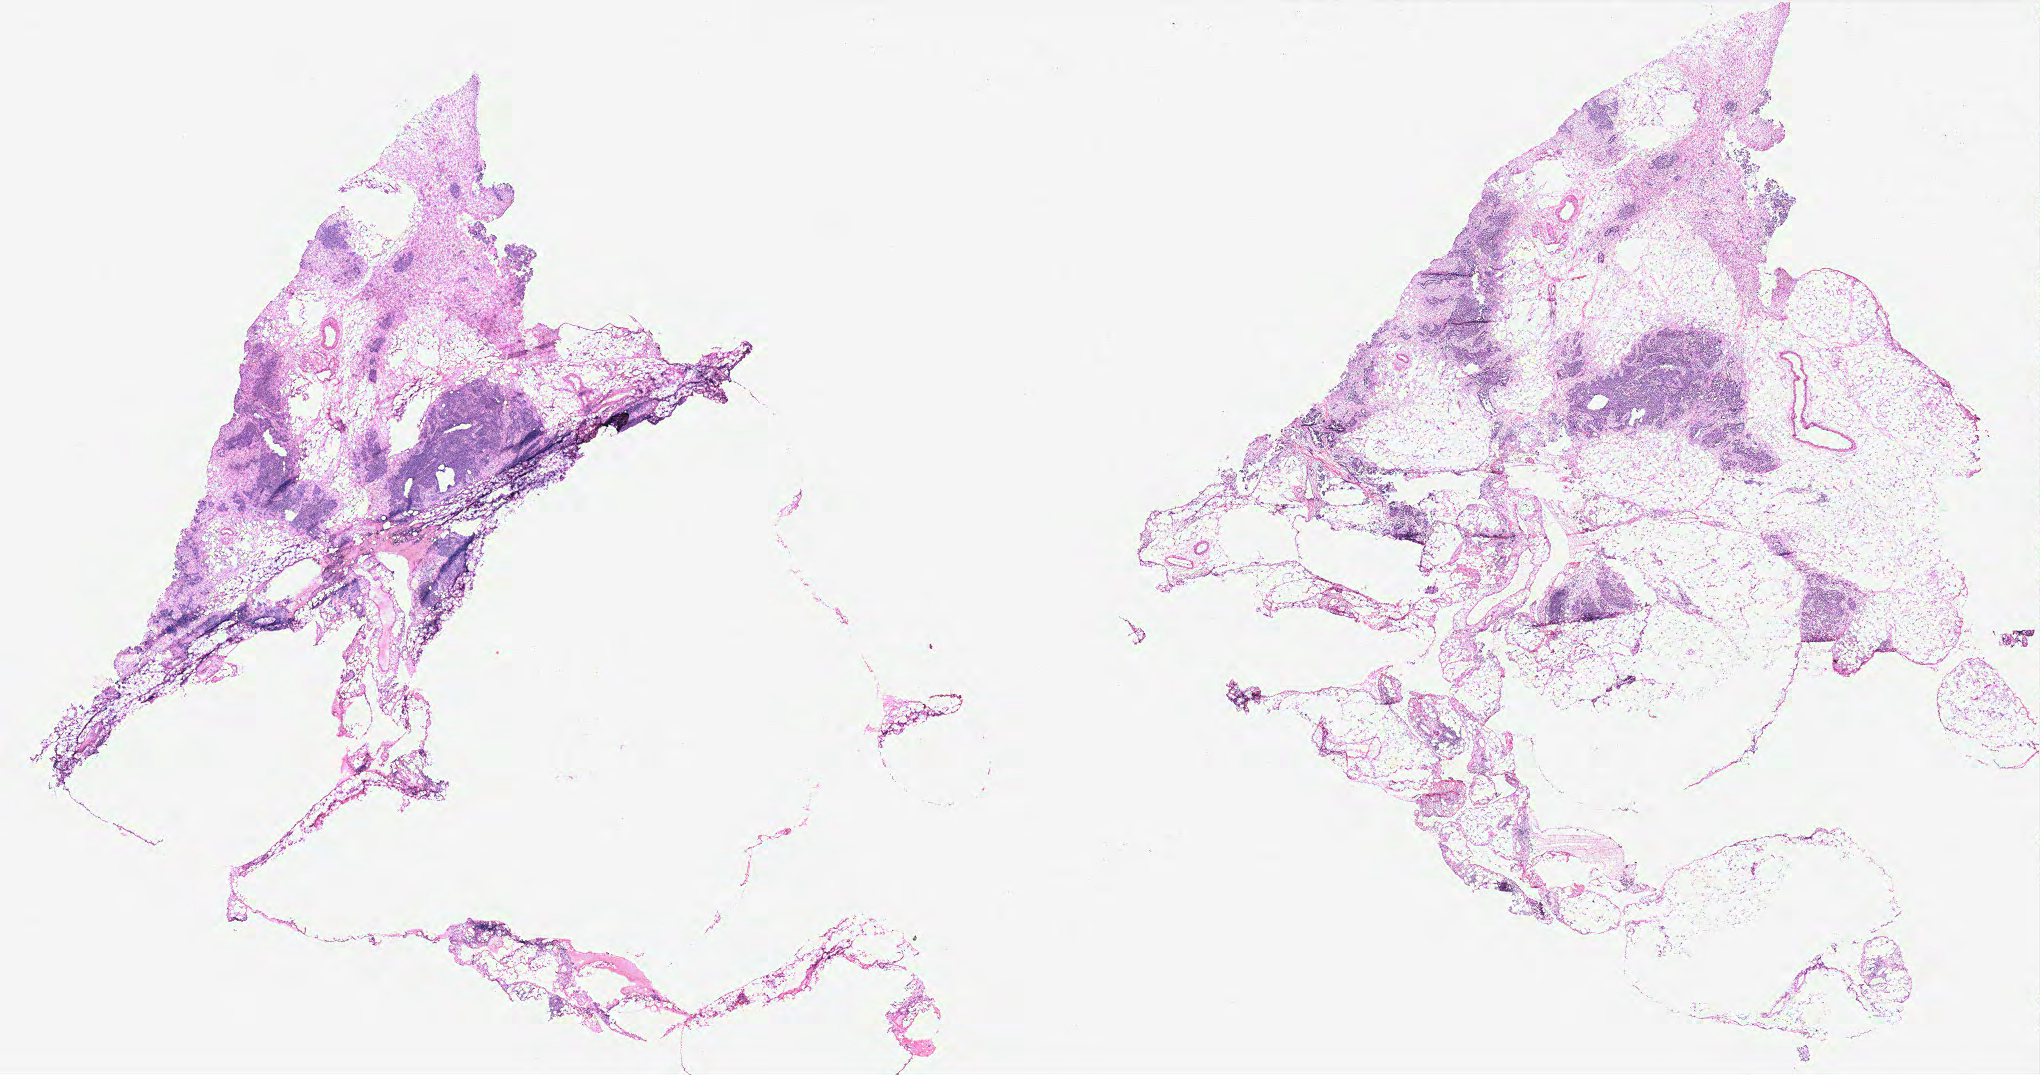
H&E-stained whole-slide image, a low-resolution overview of the entire scanned area, about 32.7 x 17.2 mm (acquisition: 40x scan), tumour tissue sample, ovary. 62-year-old female patient.
• primary tumour site (as recorded): ovary
• diagnosis: Serous adenocarcinoma, NOS